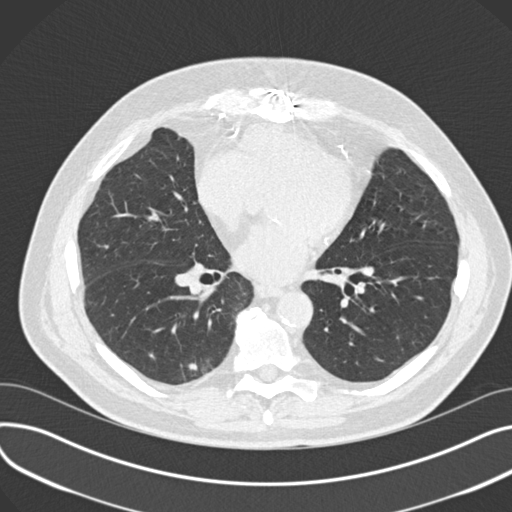
Low-dose screening chest CT, axial slice, third screening round (two years after baseline), lung window (W 1500 / L -600 HU), slice 98 of 177 in the series. Male participant, aged 68 years at enrolment. Former smoker at enrolment.
Lesion marked by an expert reader, box from (x=179, y=347) to (x=225, y=390) px. The screening reader recorded 4 non-calcified nodules or masses ≥4 mm on this exam; which of them this box marks is not recorded. Official screen result: positive, other. Participant outcome: lung cancer diagnosed 68 days after this screen — adenosquamous carcinoma, right lower lobe, moderately differentiated (G2), stage IB (AJCC 6th edition), 31 mm at pathology.